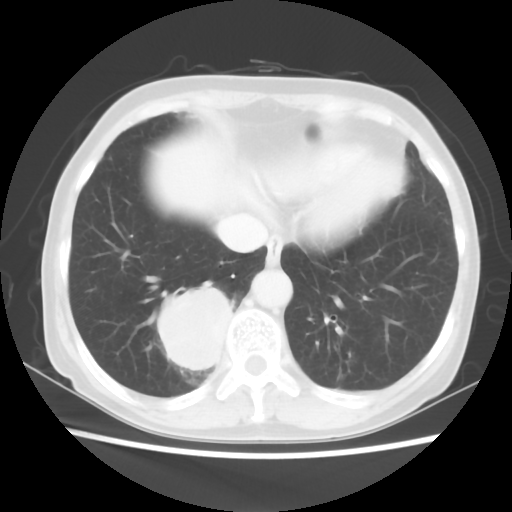
Chest CT, one axial slice. Position 15 of 56 along the scan axis. Reconstruction kernel STANDARD. Lung window (W 1500 / L -600 HU). 5 mm slice thickness. 512 × 512 image matrix. Patient: female, 66 years. From the clinical record (not read from this slice): clinical TNM (as recorded): T2 N3 M0; histopathological grade: G3.
Annotated regions visible in this slice (rectangle marked by the reading radiologist):
- lung tumour (recorded histology: small cell carcinoma): bounding box (x1, y1, x2, y2) in pixels: (150, 271, 237, 380)